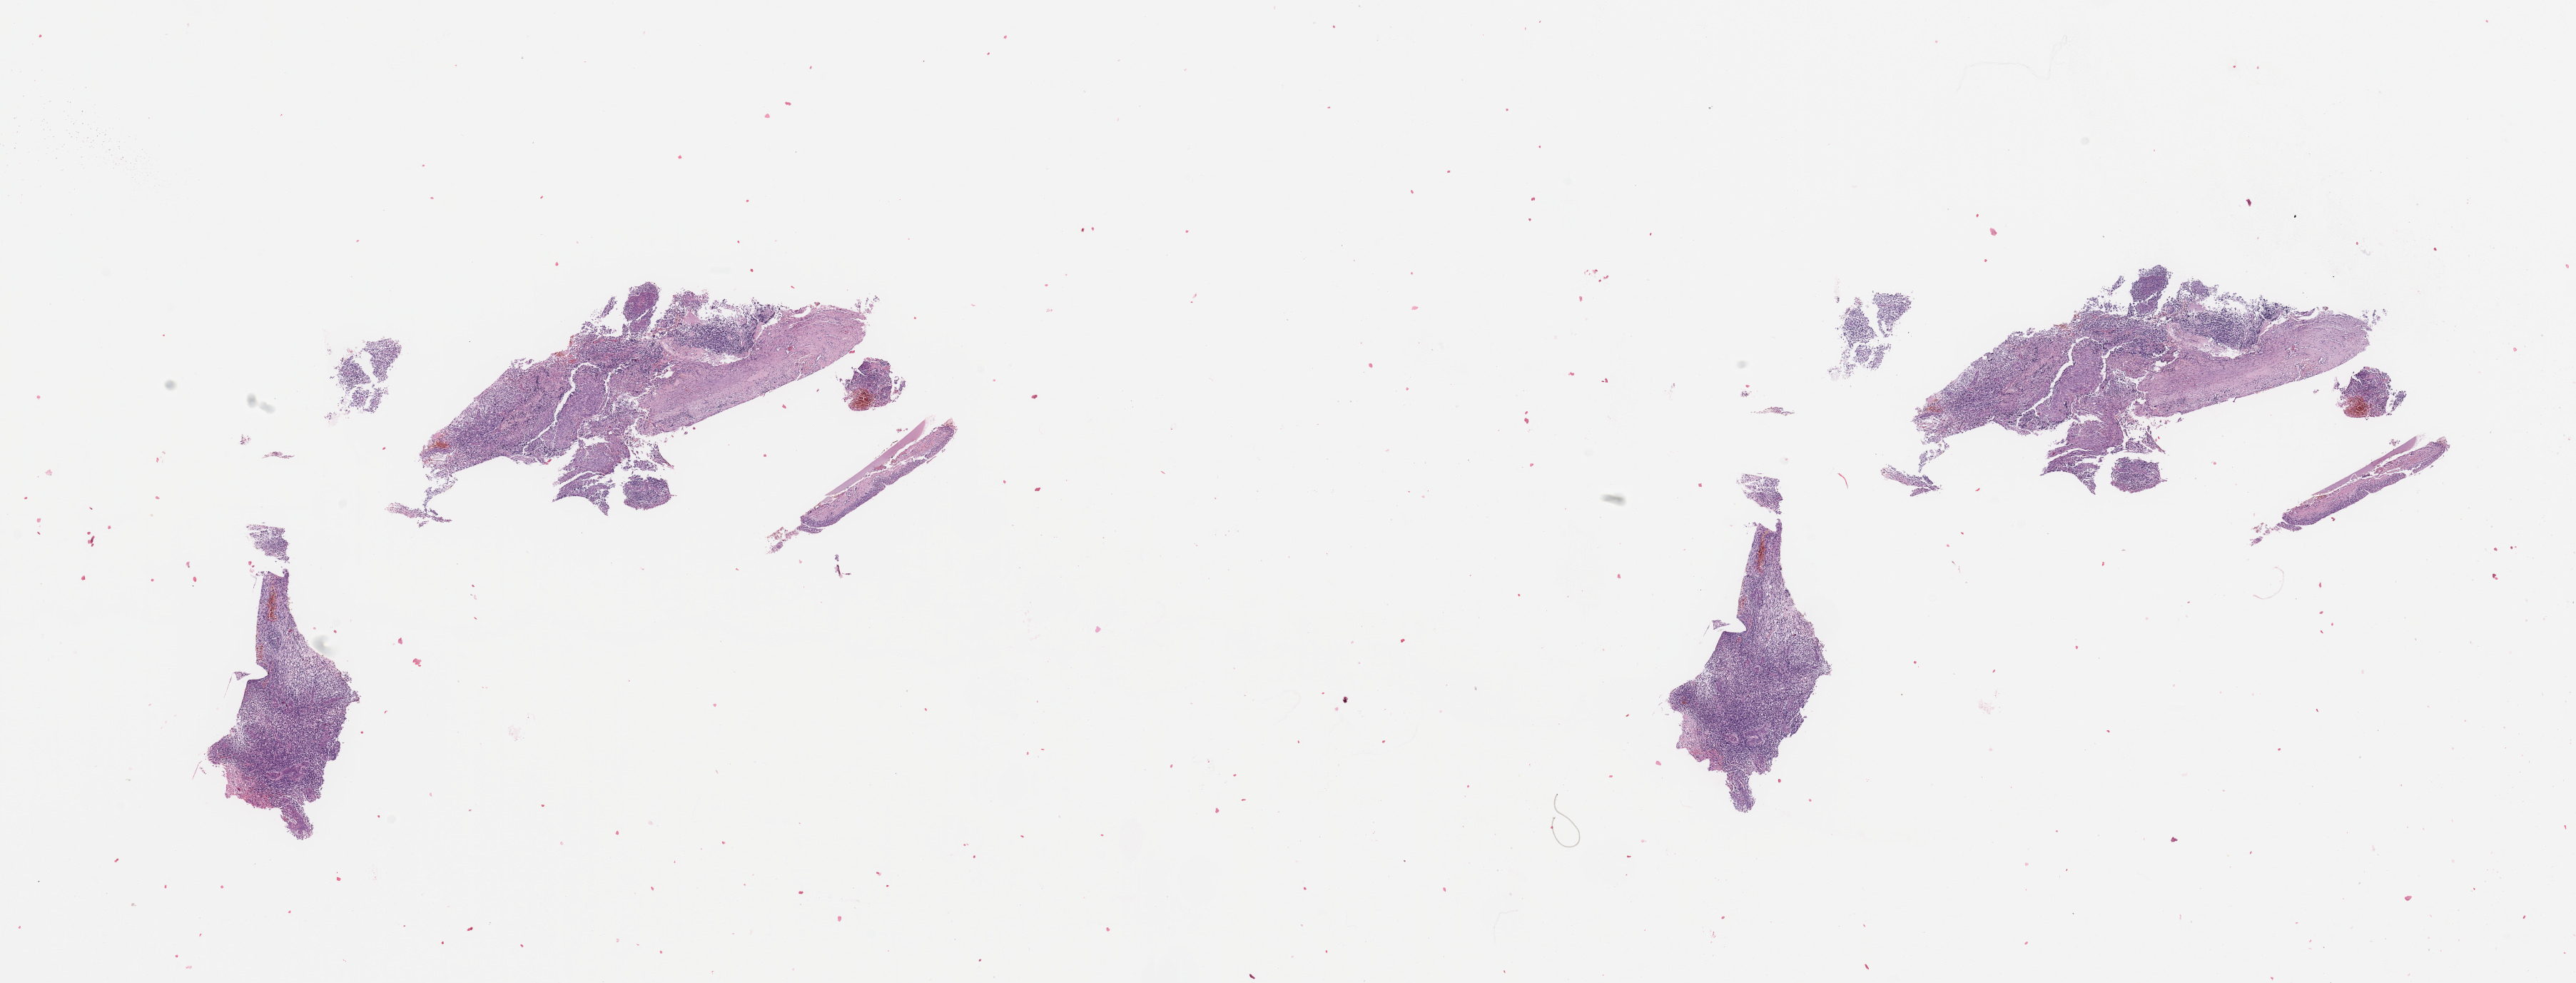
Whole-slide histology image, H&E-stained, shown as a low-resolution overview of the whole scanned area (about 28.5 x 10.9 mm, acquisition: 20x scan), brain, tumour tissue. Female, 60 y/o.
Primary tumour site (as recorded): parietal lobe. Histologic diagnosis: Glioblastoma.